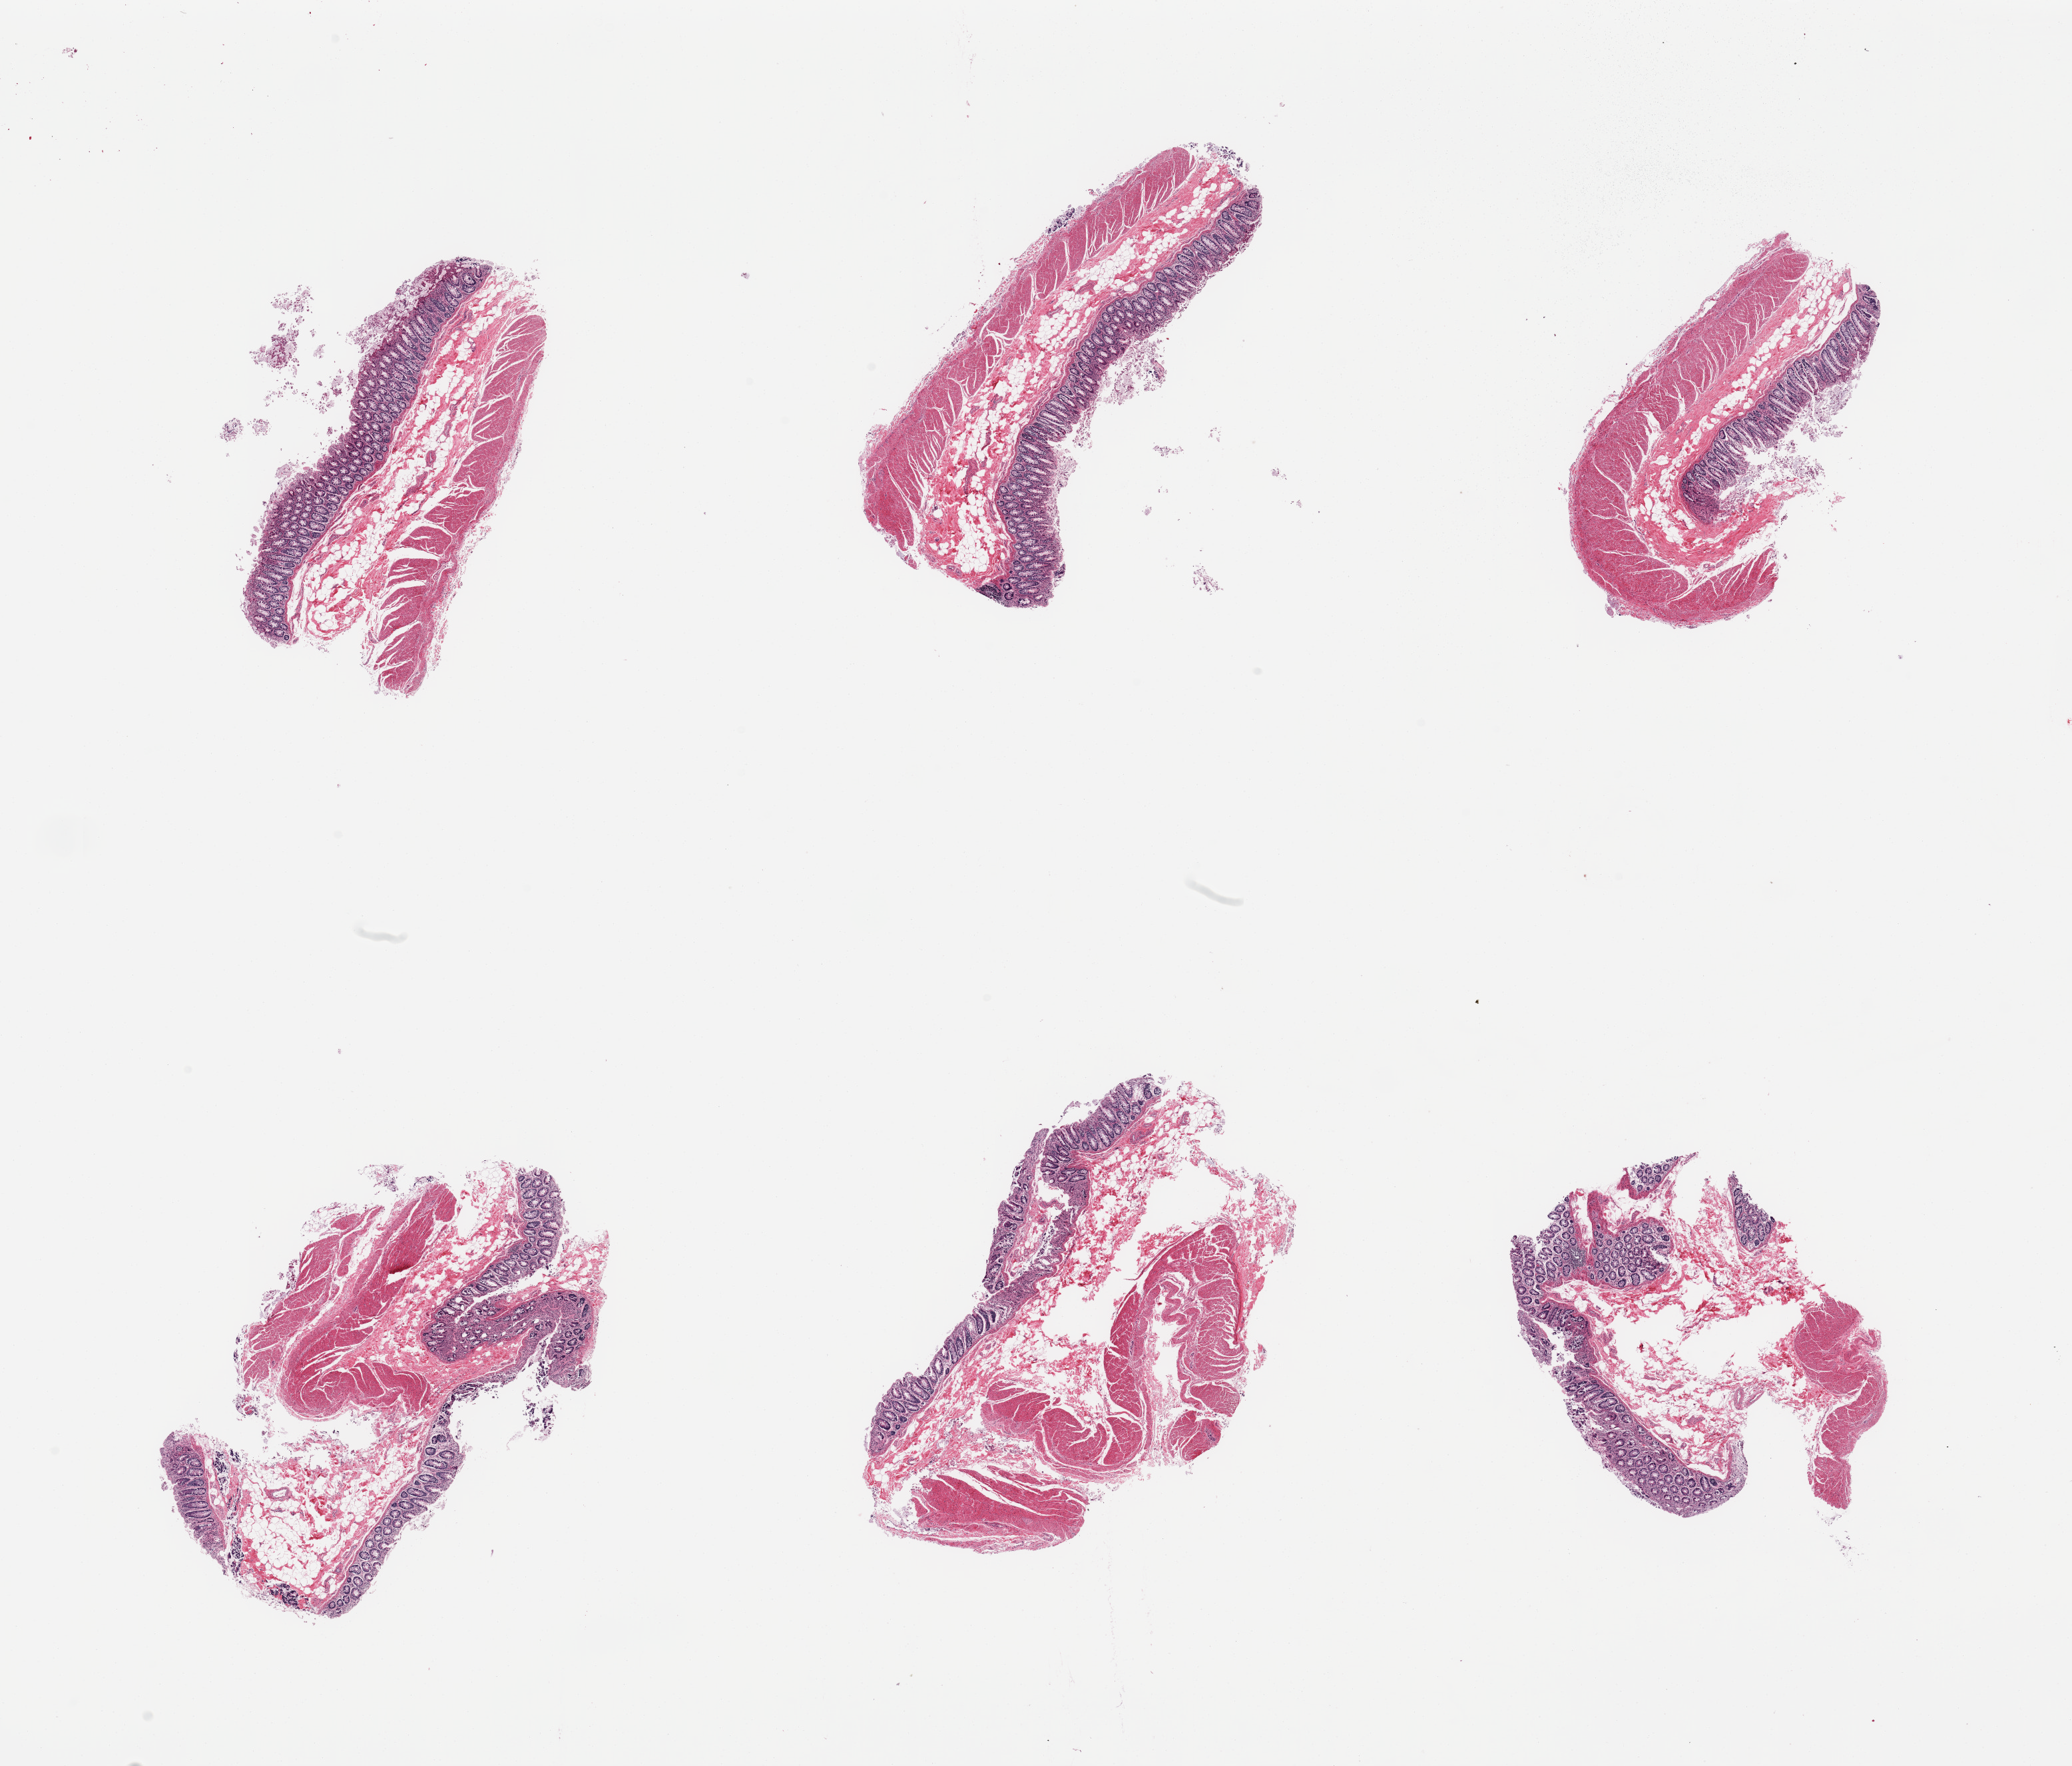
Whole-slide image, H&E stain — low-resolution overview of the scanned area, about 24.6 x 21.0 mm, PAXgene-fixed paraffin-embedded (PFPE) section, sampled site (target tissue): transverse colon, tissue donor sample. Donor: male.
Reviewer comment on this tissue sample: 6 pieces; mucosa, submucosa, muscularis.